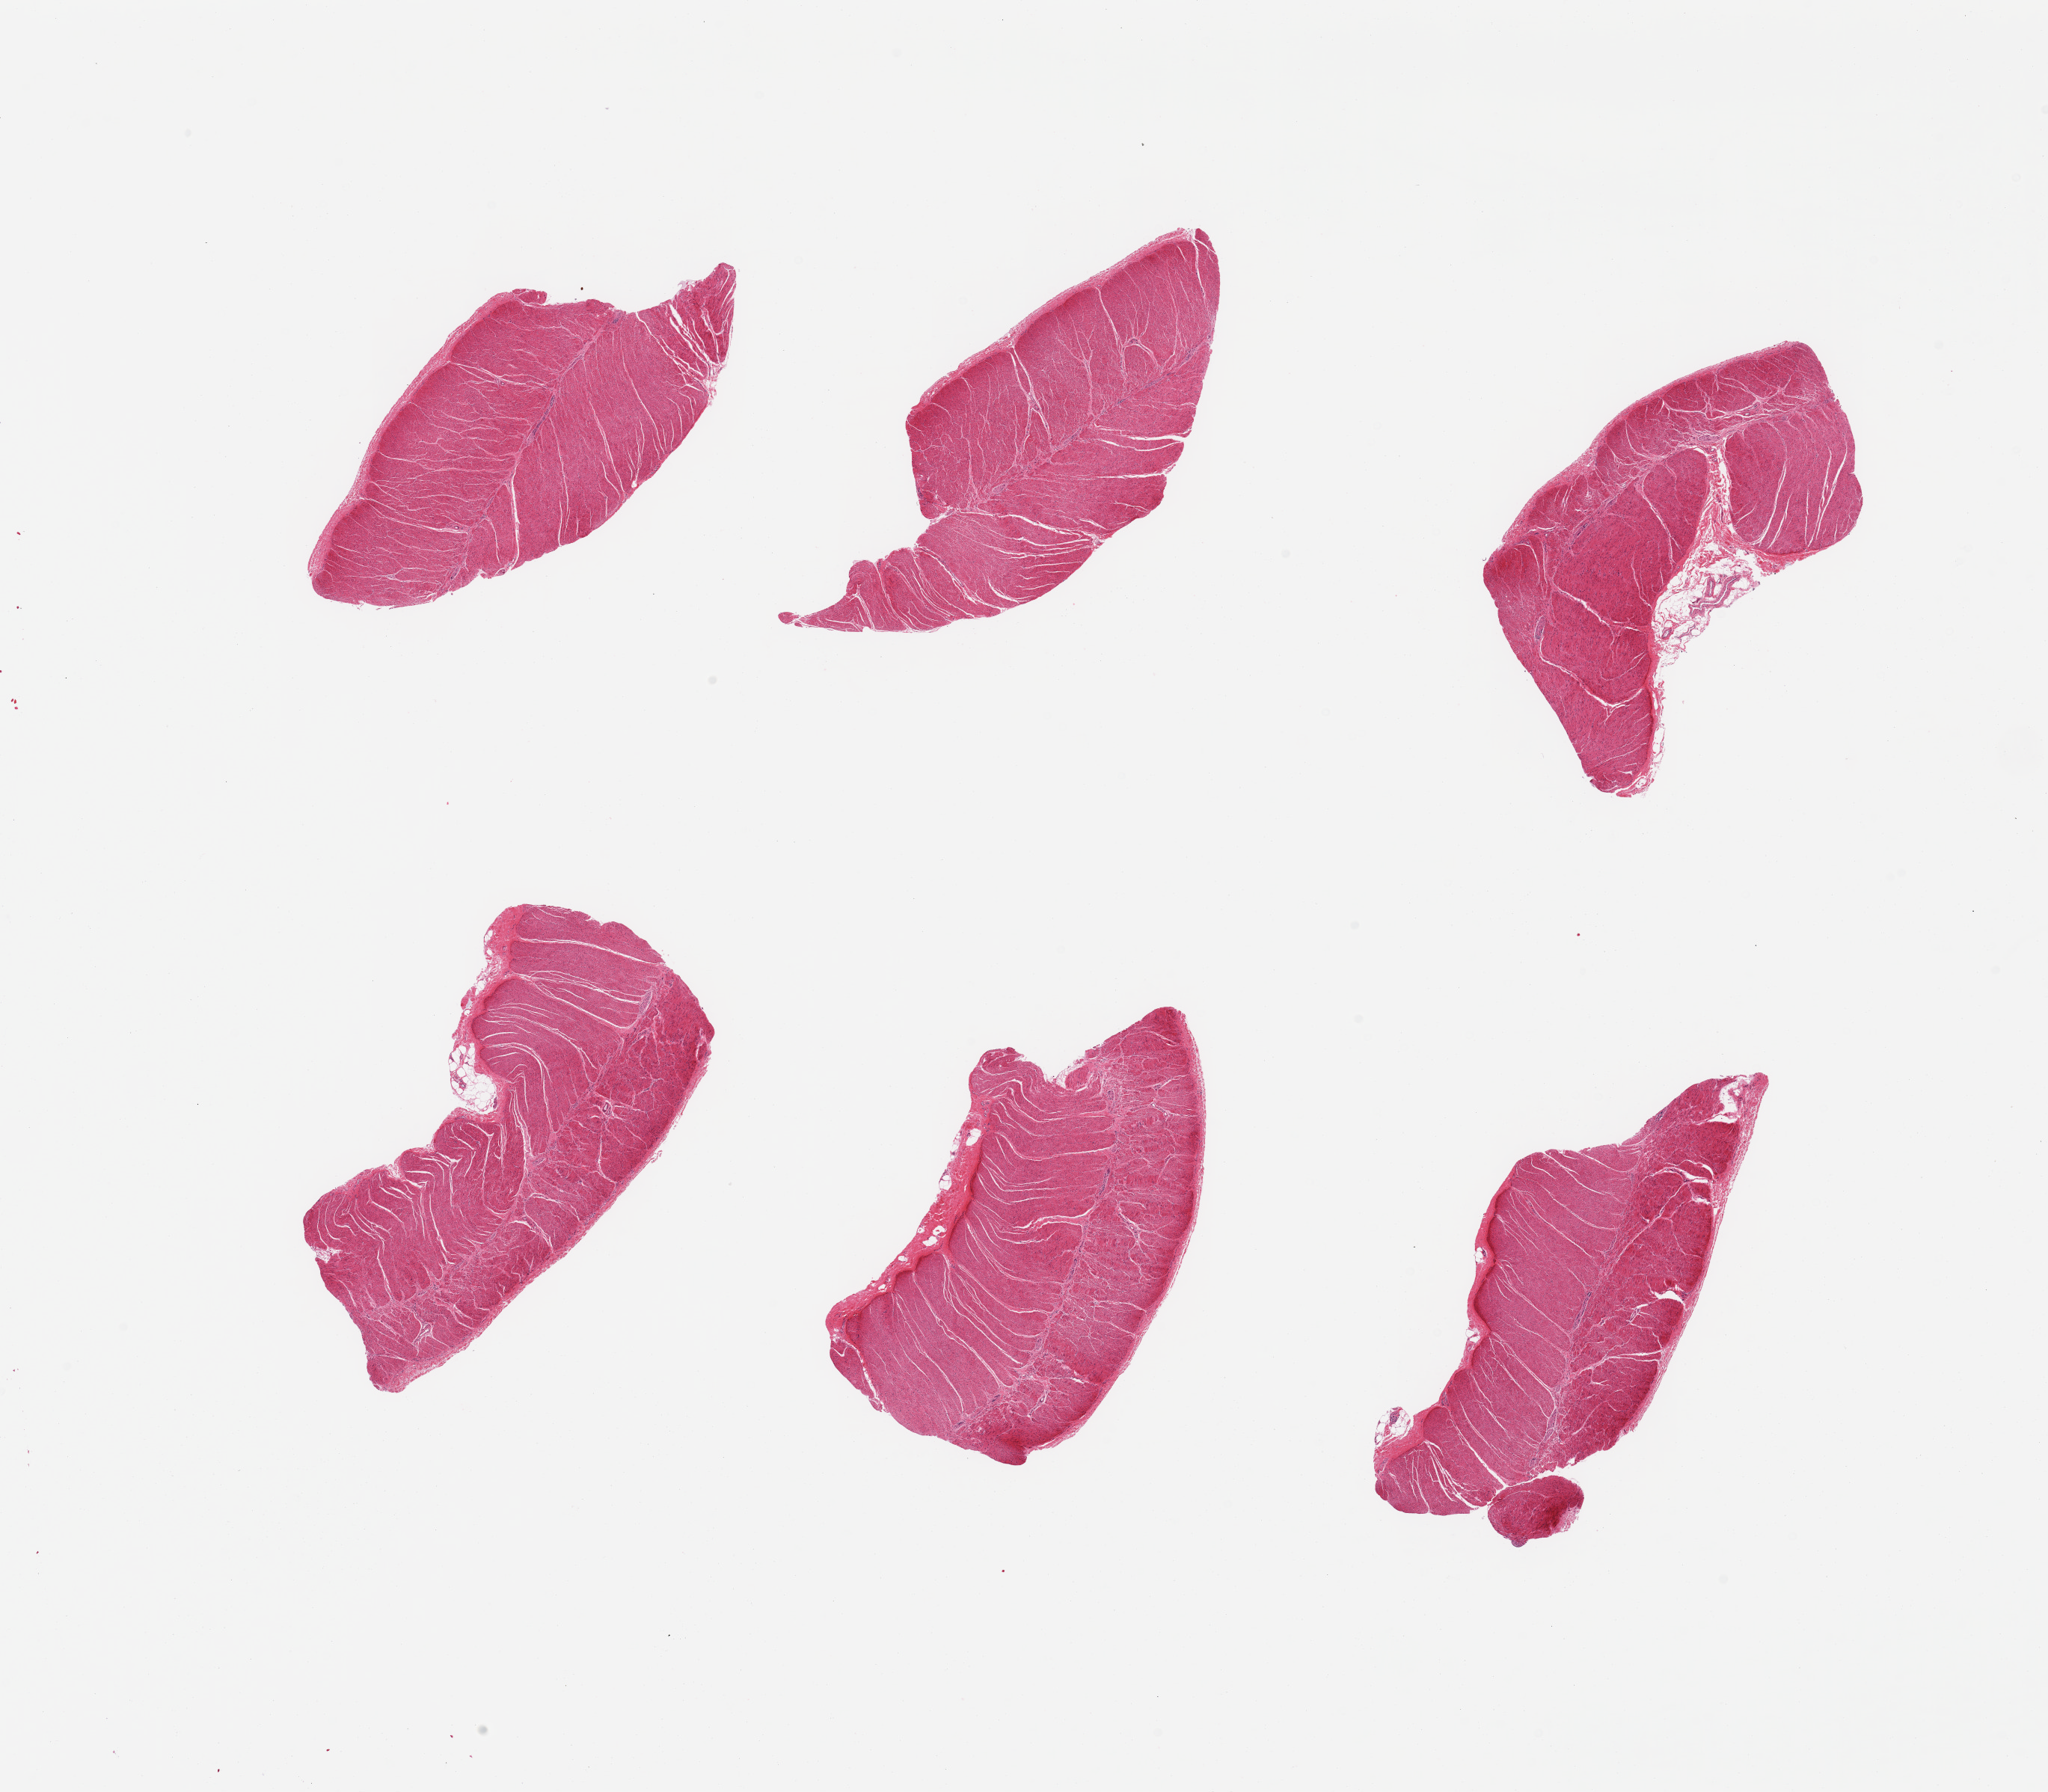
Haematoxylin and eosin whole-slide image — whole scanned area (about 21.7 x 19.0 mm, from a 20x scan) shown as a low-resolution overview, PAXgene-fixed paraffin-embedded (PFPE) section, target tissue: sigmoid colon, donor tissue sample. Male donor.
- reviewer comment on this tissue sample: 6 pieces, confirmed target muscularis